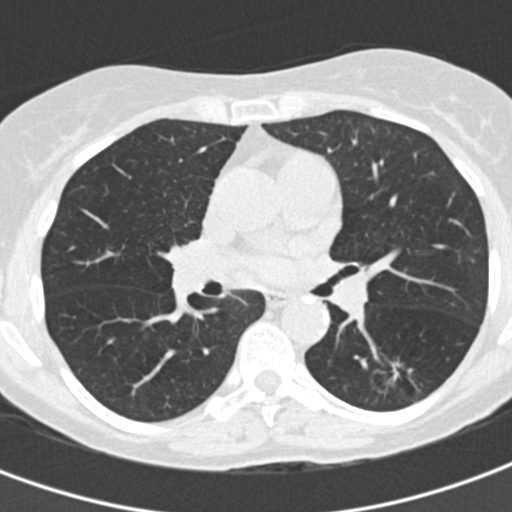
Low-dose screening chest CT, one axial slice; position 86 of 155 along the scan axis; reconstruction kernel B30f; 120 kVp; lung window (W 1500 / L -600 HU); 2 mm slice thickness; 512 × 512 image matrix.
Structures marked on this image (manually delineated by an expert):
- lesion 1 (tumor, lower lobe of left lung): box from (x=387, y=359) to (x=413, y=386) px